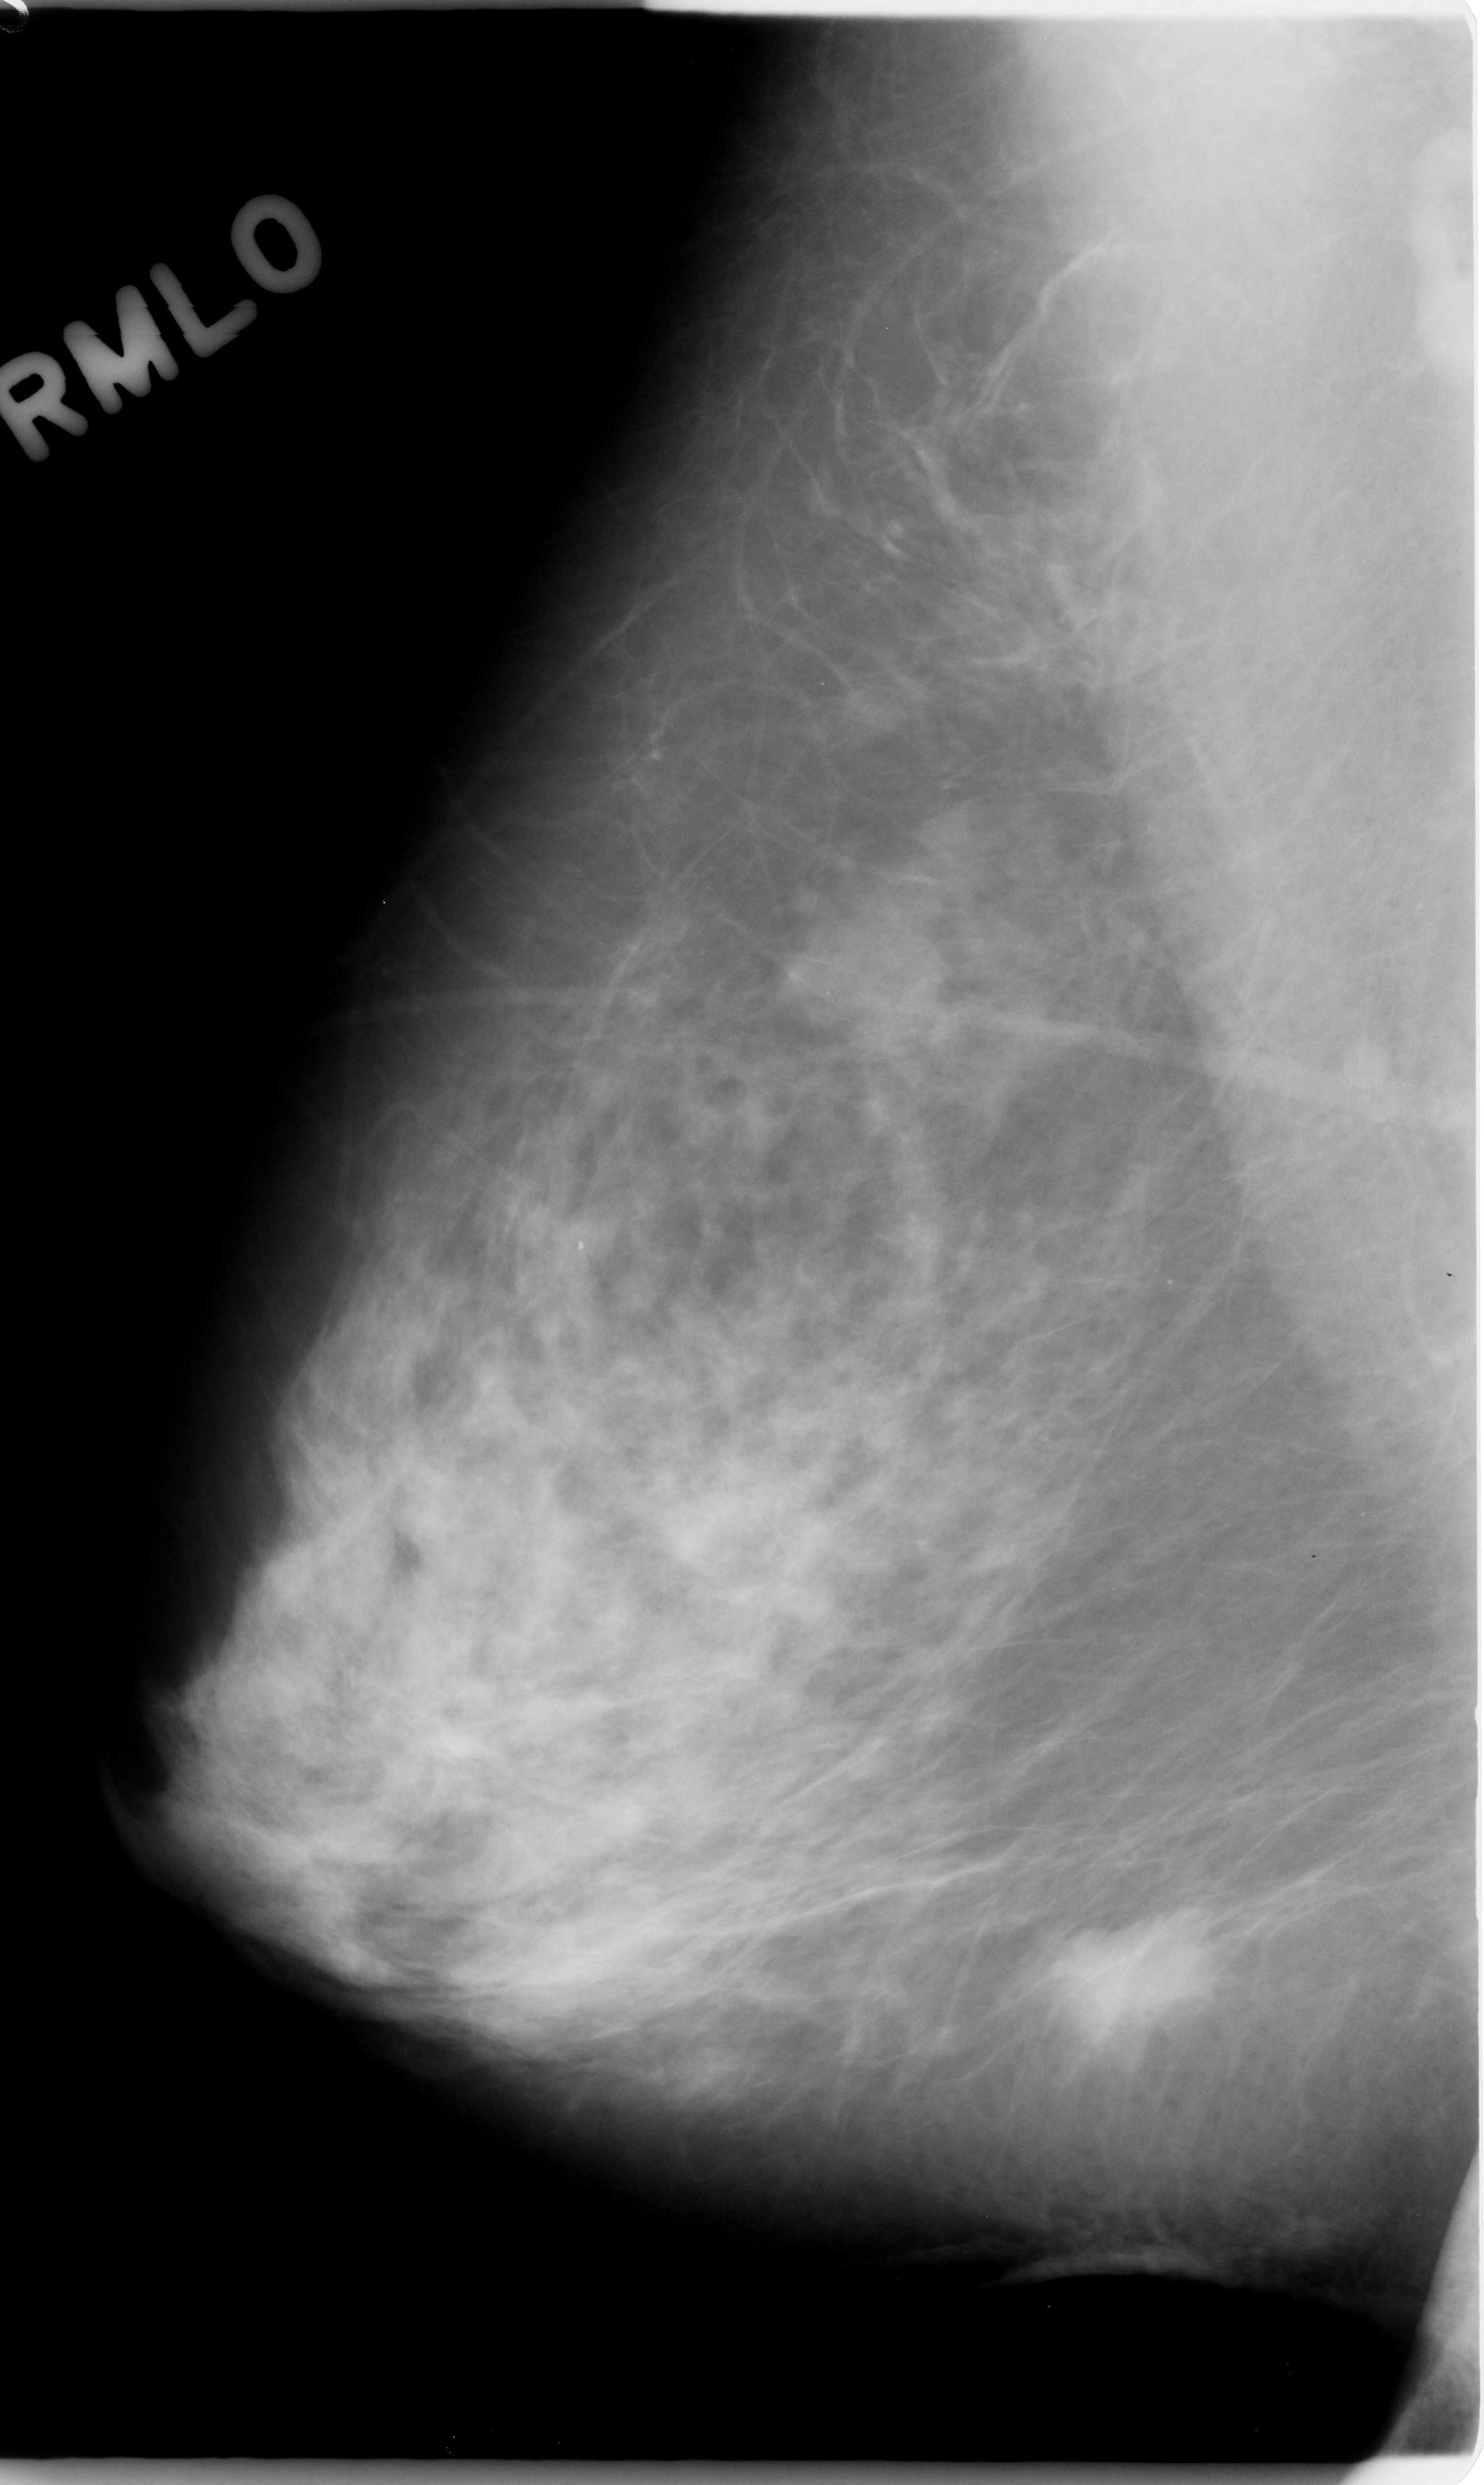
Digitized screen-film mammogram. Right breast. MLO view. BI-RADS breast density category 2 (scale 1–4). 1484 × 2485 image matrix.
Expert-marked regions of interest on this image (one box per marked abnormality):
- mass, shape irregular, margins spiculated; BI-RADS assessment category 5; pathology (as recorded): malignant: bounding box [x1, y1, x2, y2] px = [1058, 1895, 1237, 2064]